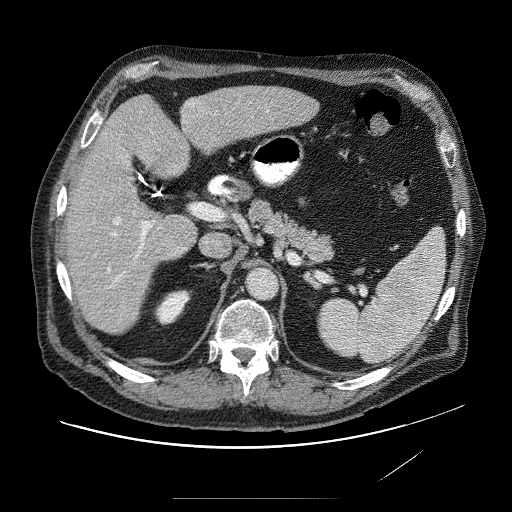
Contrast-enhanced abdominal CT (liver protocol), one axial slice; reconstruction kernel STANDARD; soft-tissue window (W 400 / L 40 HU); 512 × 512 image matrix, field of view 420 × 420 mm. From the clinical record (not read from this slice): diagnosis: hepatocellular carcinoma (patient treated with transarterial chemoembolisation; whether this scan precedes or follows treatment is not stated here); TNM stage (as recorded): Stage-IVA; Child-Pugh class: A; tumour differentiation: moderately differentiated; tumour nodularity: multinodular.
Annotated regions visible in this slice (semi-automatically segmented with operator editing):
- liver parenchyma outside the tumour (the mass and vessels are separate outlines, so this box may not span the whole liver): bounding box [x1, y1, x2, y2] px = [62, 84, 324, 334]
- mass: [164, 235, 196, 261]
- liver vessels: [96, 111, 259, 290]